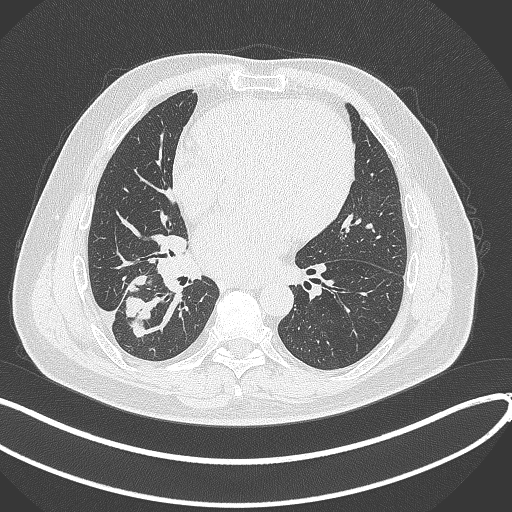
Chest CT, one axial slice; reconstruction kernel B70f; lung window (W 1500 / L -600 HU); 512 × 512 image matrix, field of view 400 × 400 mm. Patient: male, 59 years.
Annotated regions visible in this slice (bounding box drawn by a radiologist):
- lung tumour (recorded histology: adenocarcinoma): bounding box [x1, y1, x2, y2] px = [124, 271, 165, 338]